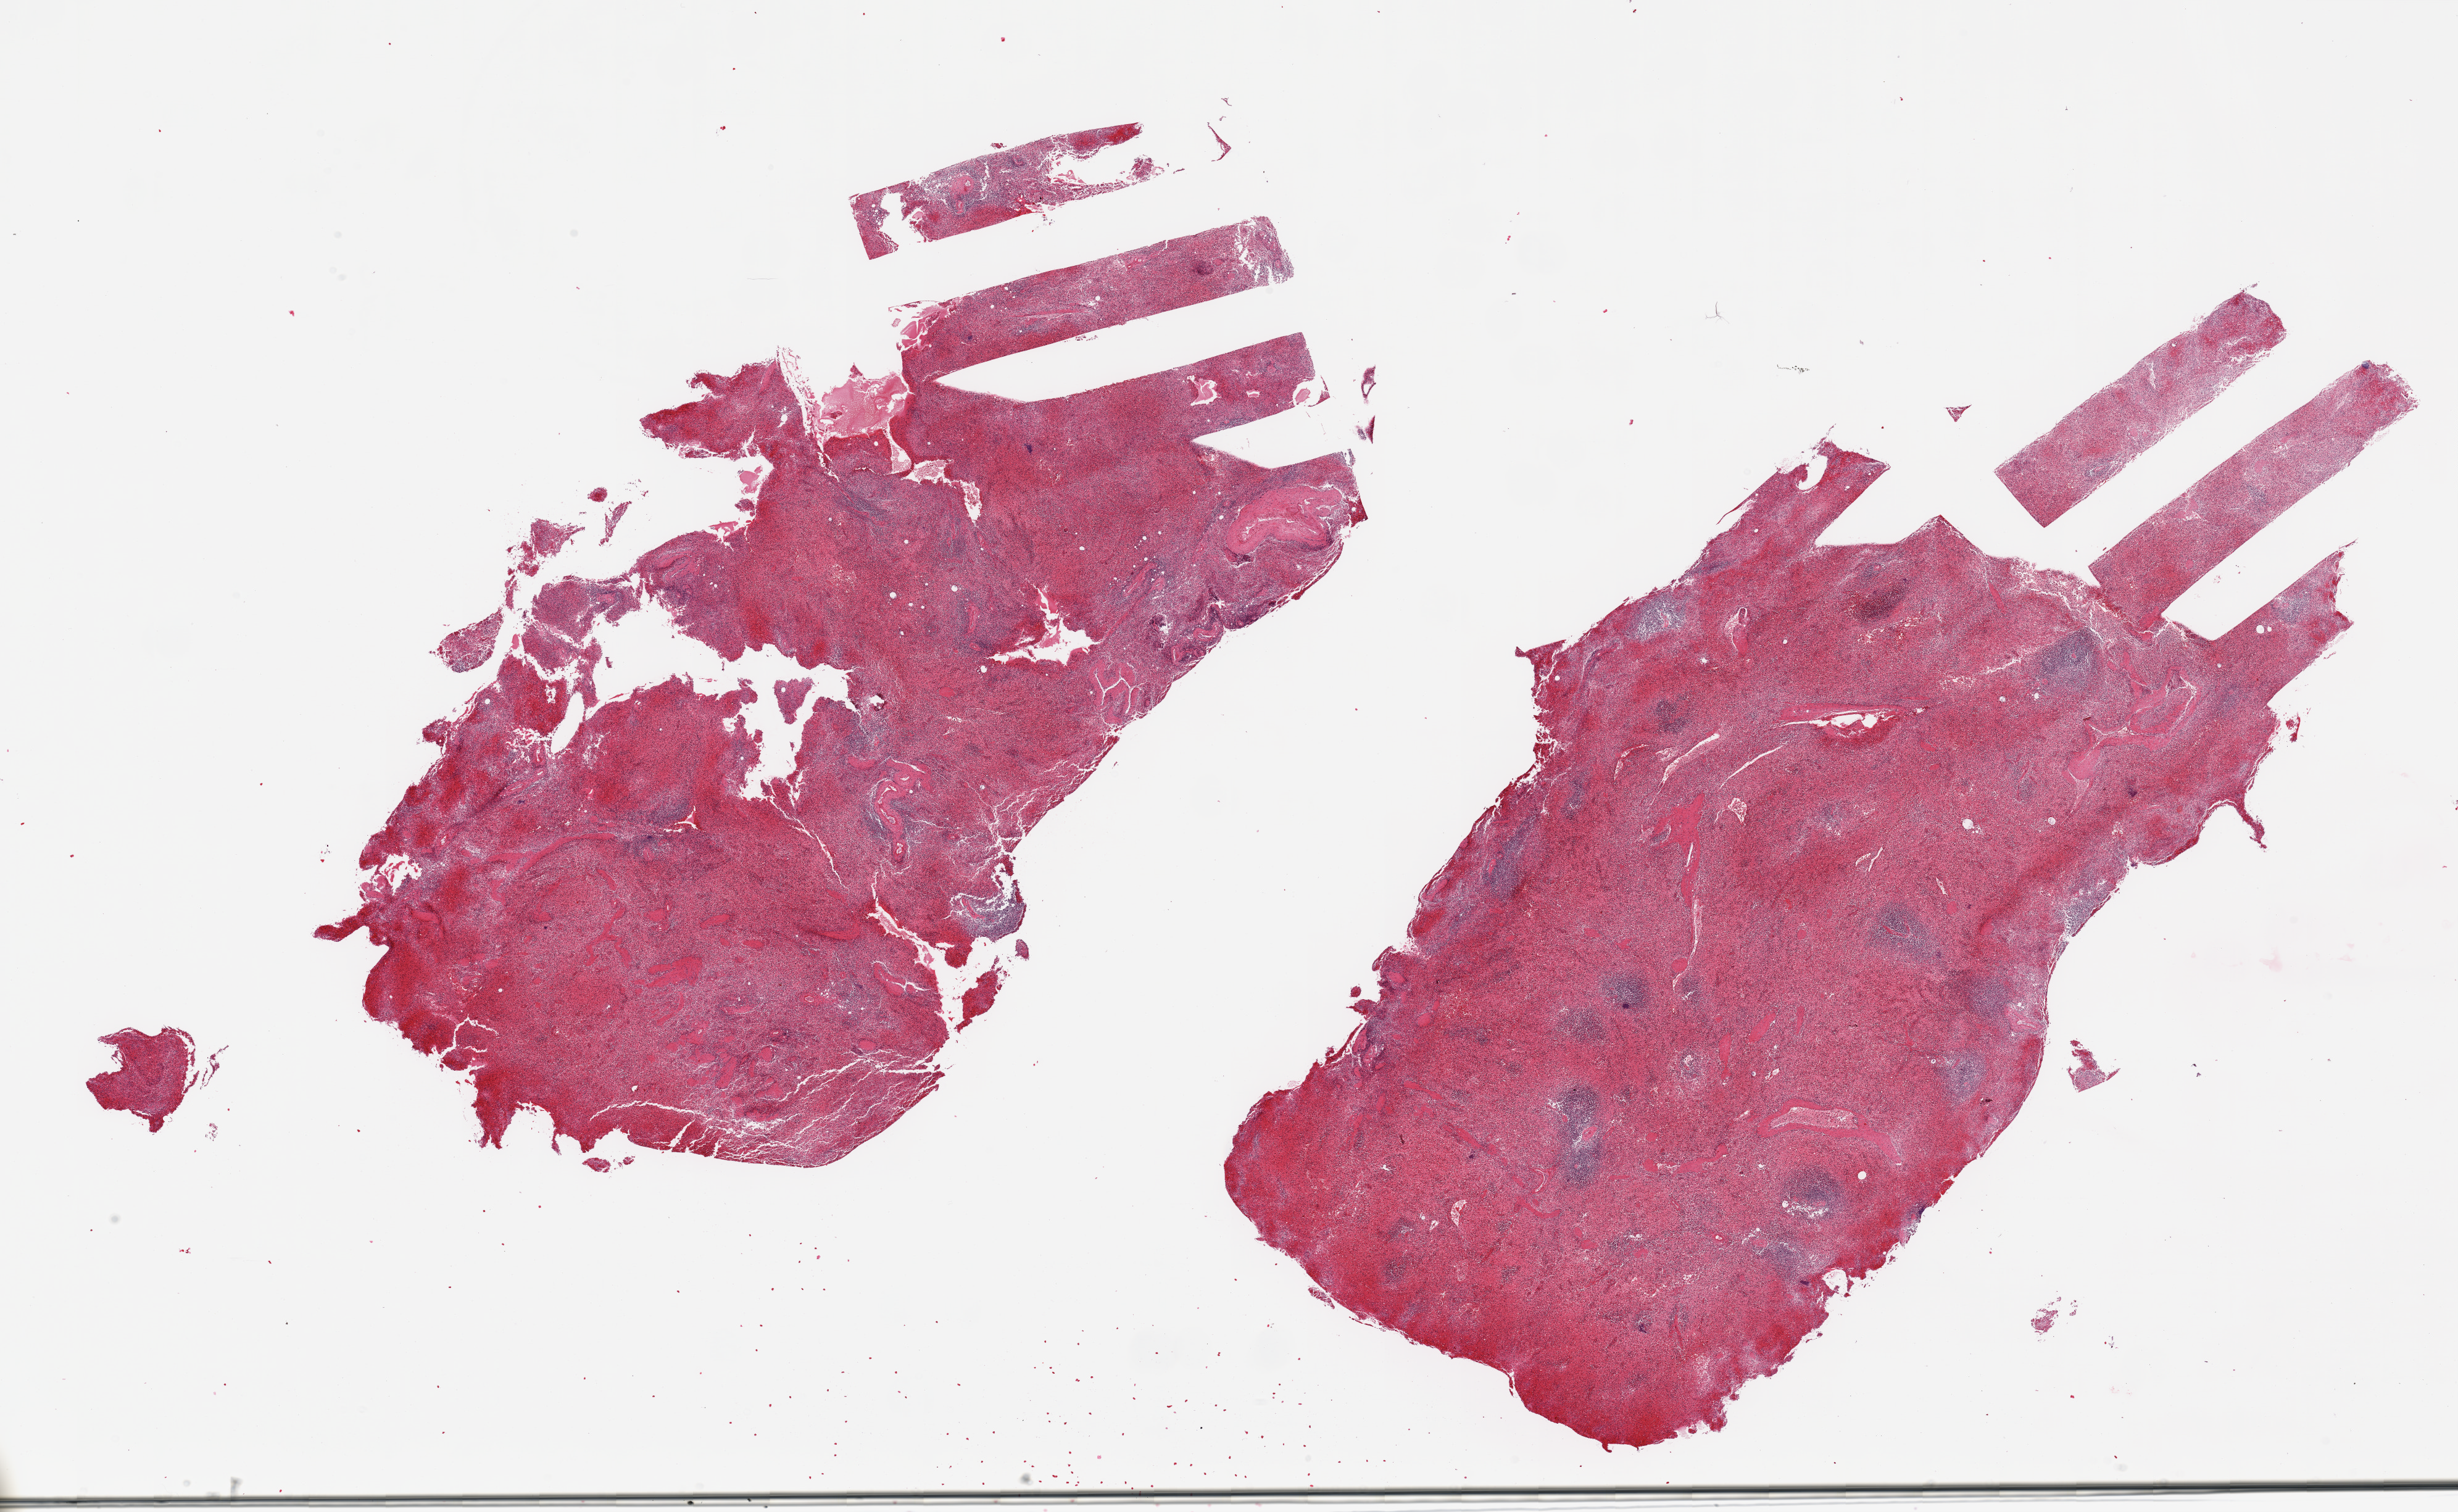
Whole-slide image, hematoxylin and eosin (H&E) stain, whole scanned area (about 31.5 x 19.4 mm) shown as a low-resolution overview; PAXgene-fixed, paraffin-embedded tissue; target tissue: spleen; donor tissue sample. Male donor.
* pathologist's review note for this sample: 2 pieces; oversized, congestion